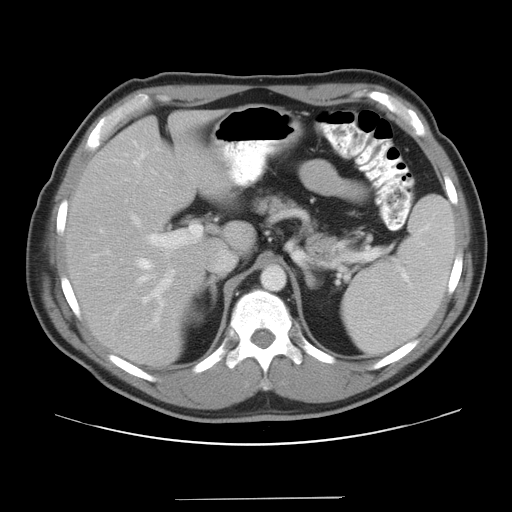
Contrast-enhanced abdominal CT, one axial slice; slice 26 of 37 in the series (ordered by position); intravenous contrast given; soft-tissue window (W 400 / L 40 HU); 512 × 512 image matrix. Male patient, age 46 years. Case-level facts recorded for this patient, not image findings: diagnosis: colorectal cancer liver metastases, imaged before liver resection; multiple liver metastases: yes; largest metastasis: 1 cm; chemotherapy before resection: yes.
Outlined on this slice (outlined manually by an expert reader):
- hepatic veins: bounding box [x1, y1, x2, y2] px = [135, 257, 156, 285]
- liver: [68, 116, 247, 367]
- planned liver remnant (the part of the liver to remain after resection): [68, 117, 248, 367]
- portal vein (with intrahepatic branches): [131, 215, 203, 329]